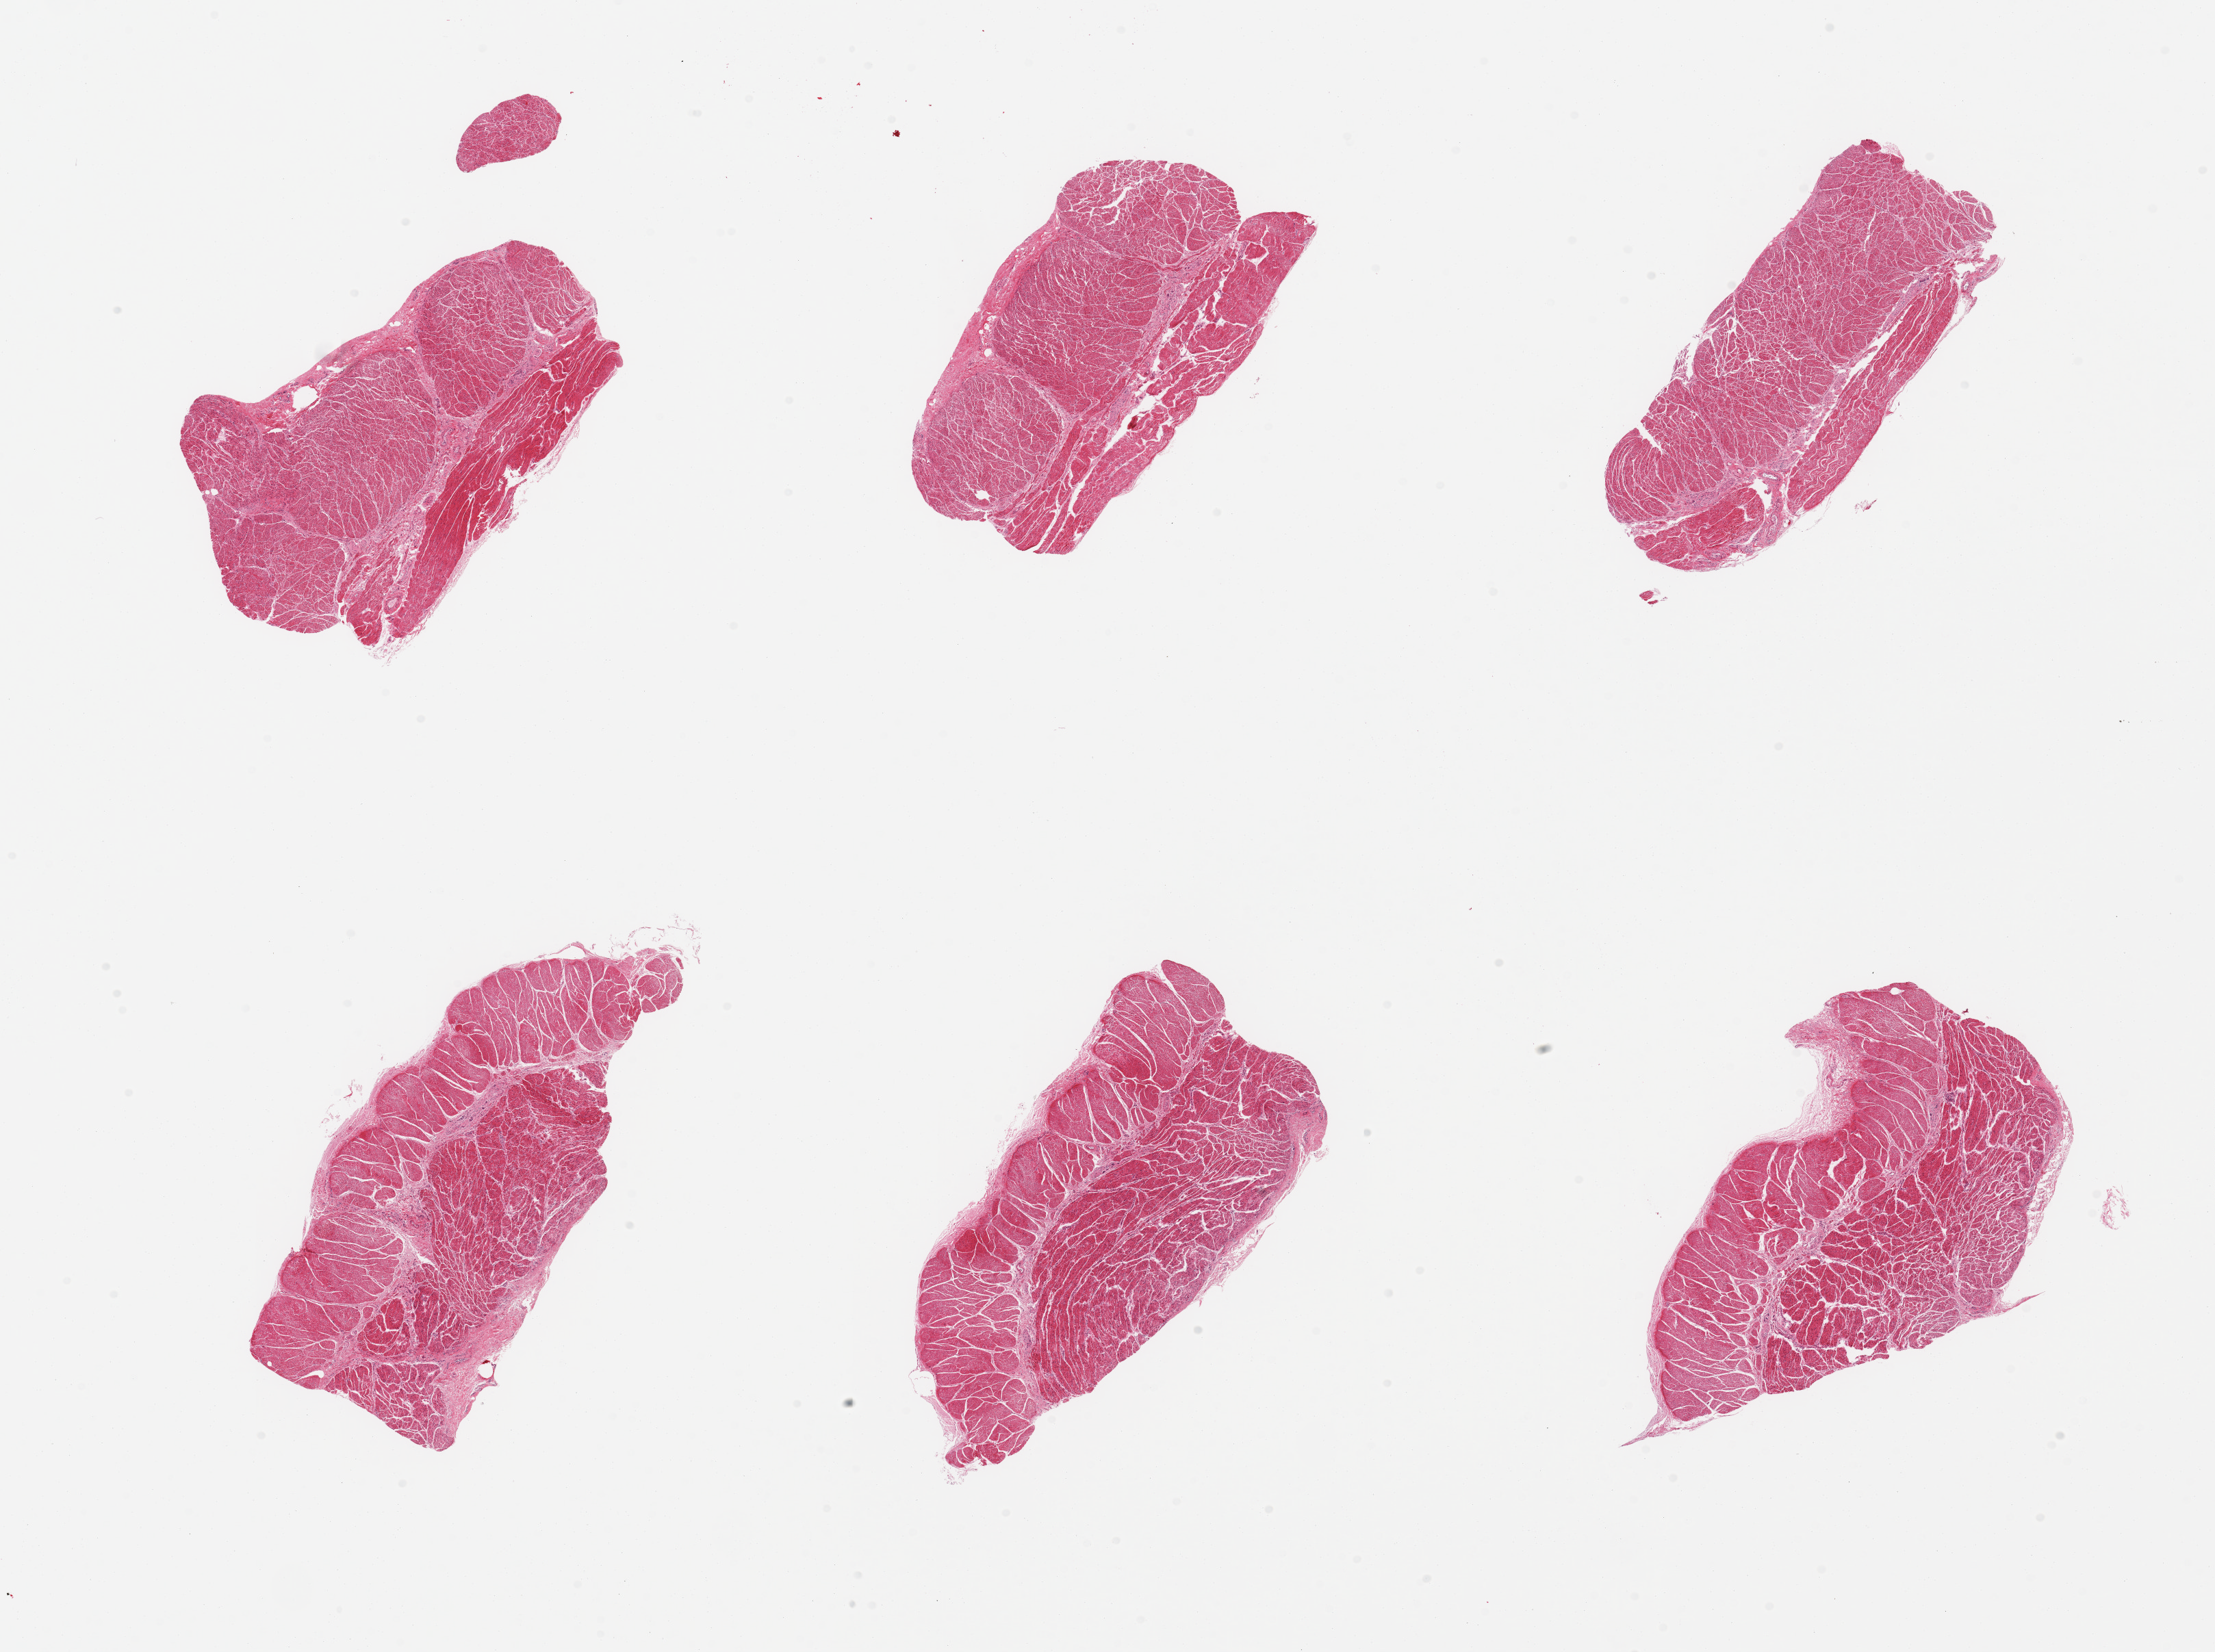
Whole-slide image, H&E stain, a low-resolution overview of the entire scanned area, about 25.6 x 19.1 mm (acquisition: 20x scan). PAXgene-fixed paraffin-embedded (PFPE) section. Target tissue: esophageal muscle. Tissue donor sample. Donor: male.
• reviewer comment on this tissue sample: 6 pieces, confirmed target muscularis